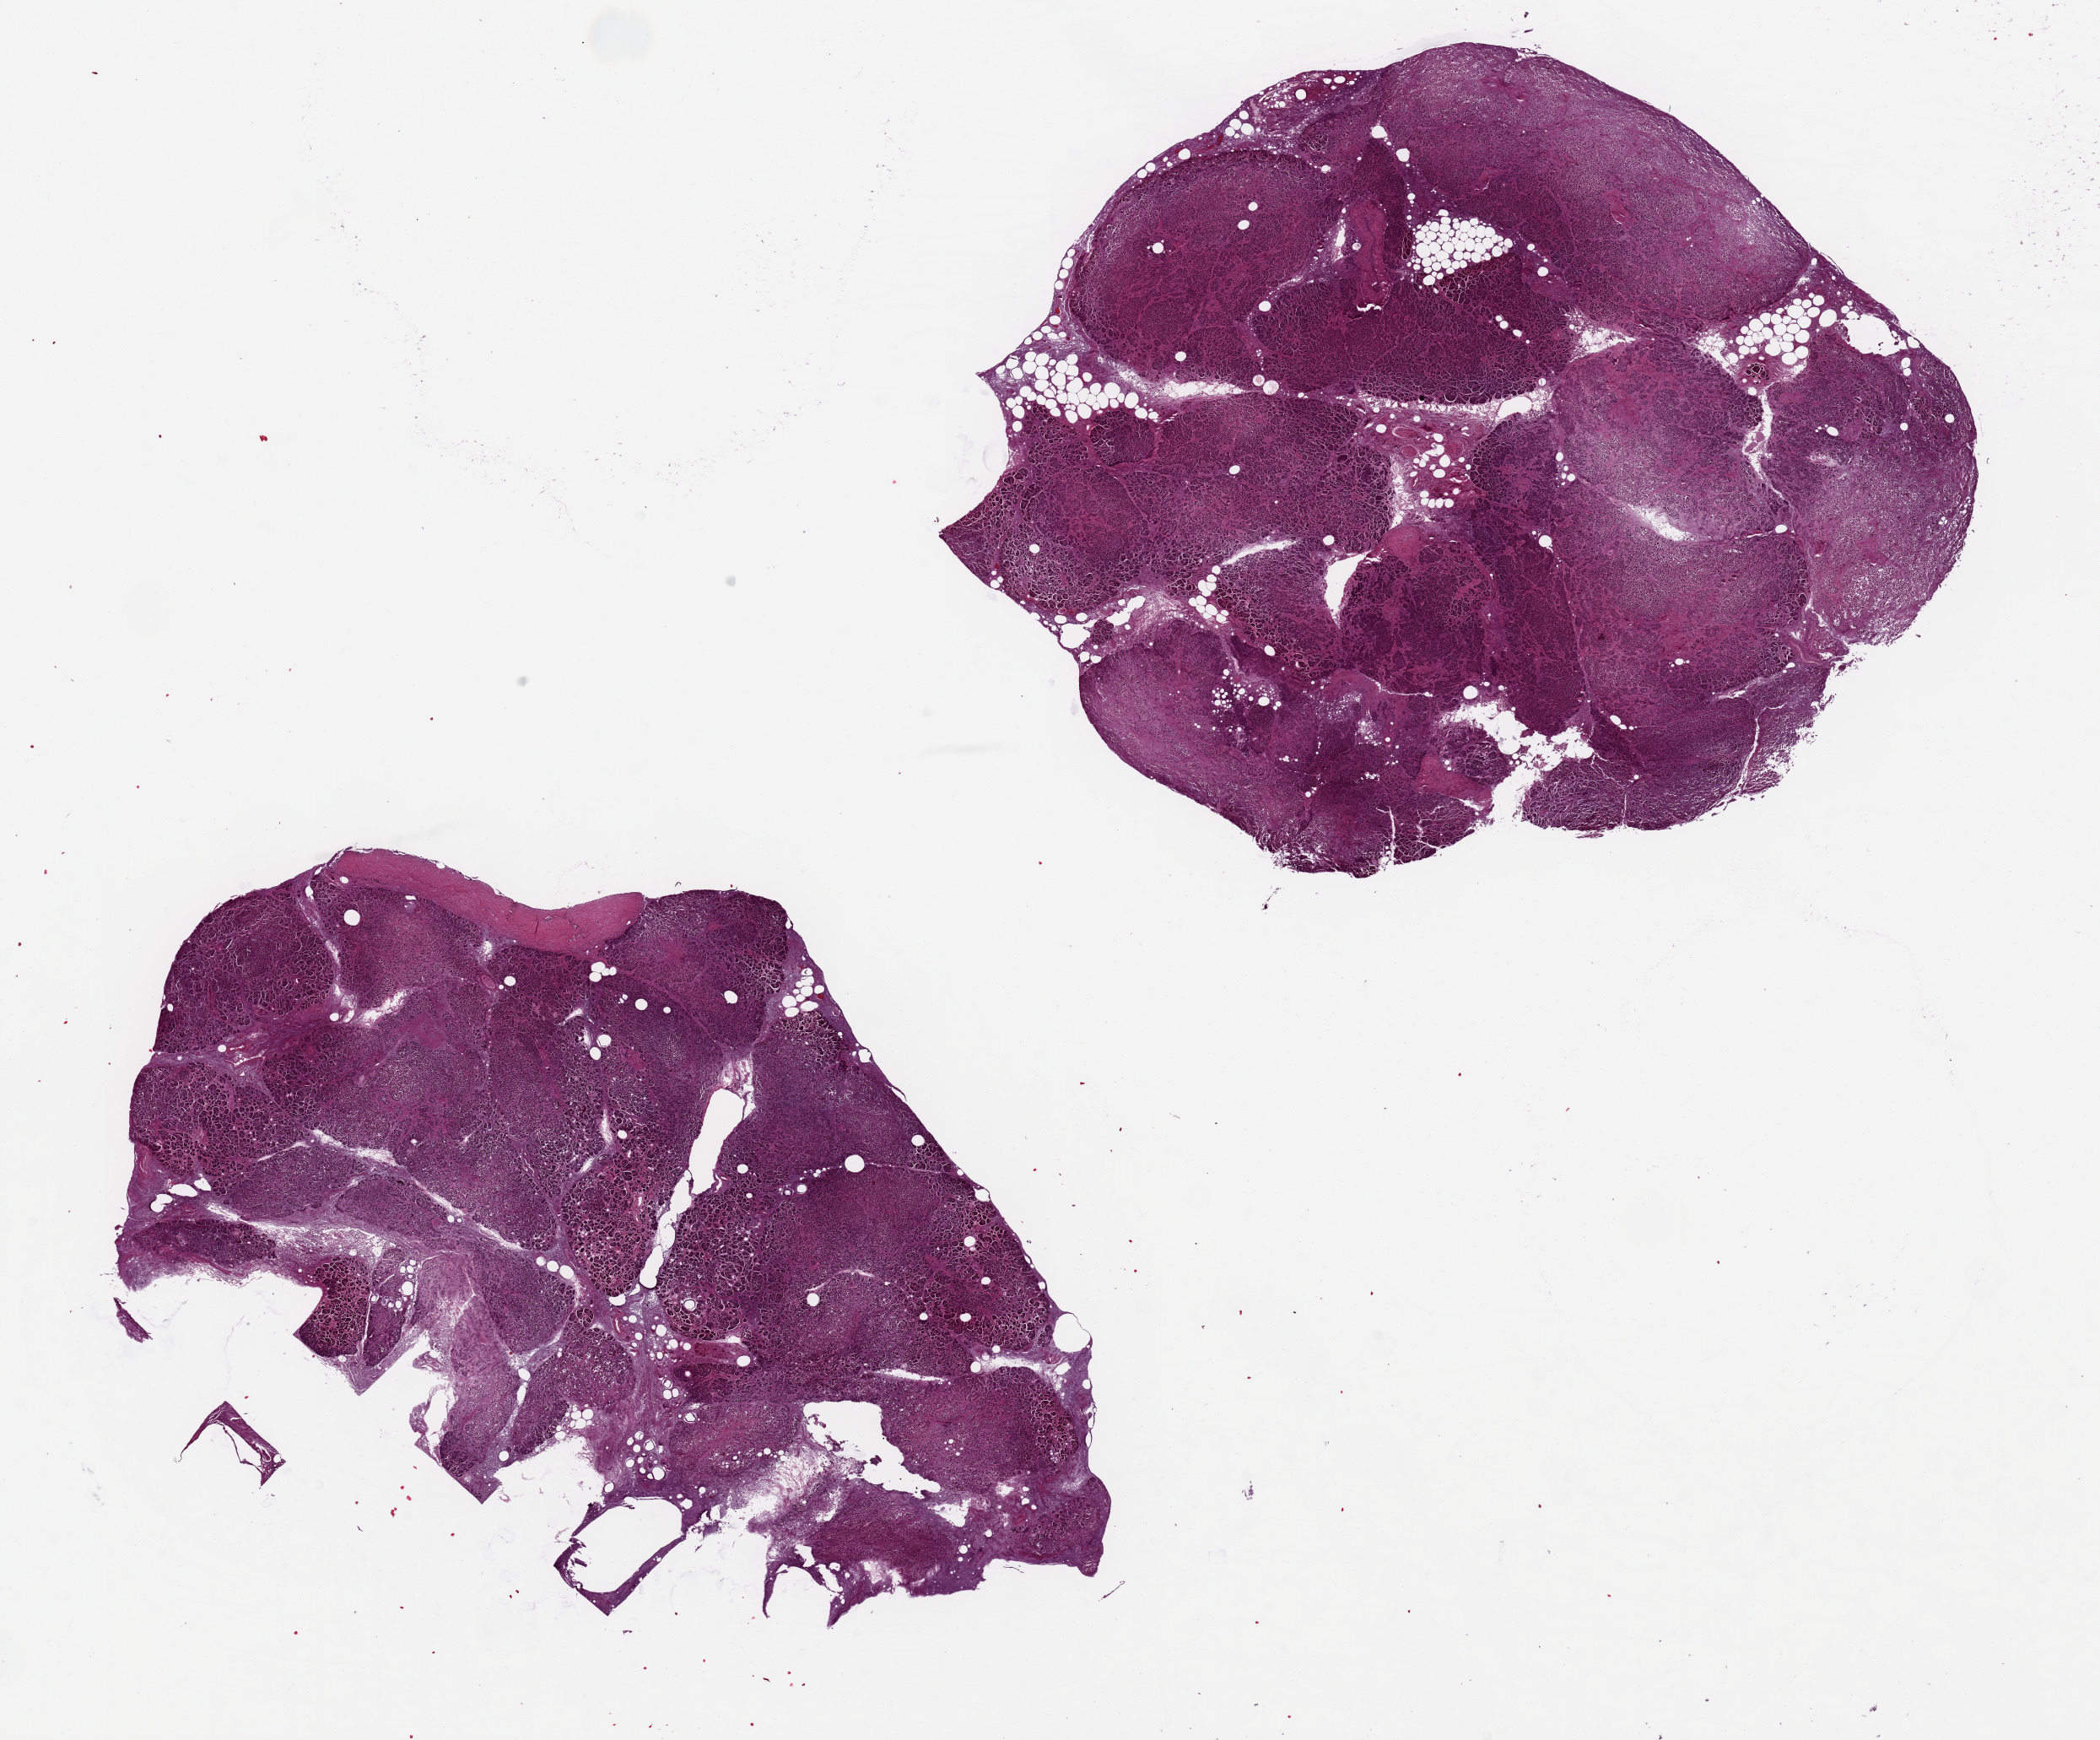
Whole-slide image, H&E stain, brightfield — low-resolution overview of the scanned area, about 19.7 x 16.3 mm, PAXgene-fixed, paraffin-embedded tissue, sampled site (target tissue): pancreas, donor tissue sample. Donor sex: male.
Pathologist's review note for this sample: 2 aliquots, ~9x7mm. ~10% interstitial fat, marked saponification, poorly preserved.